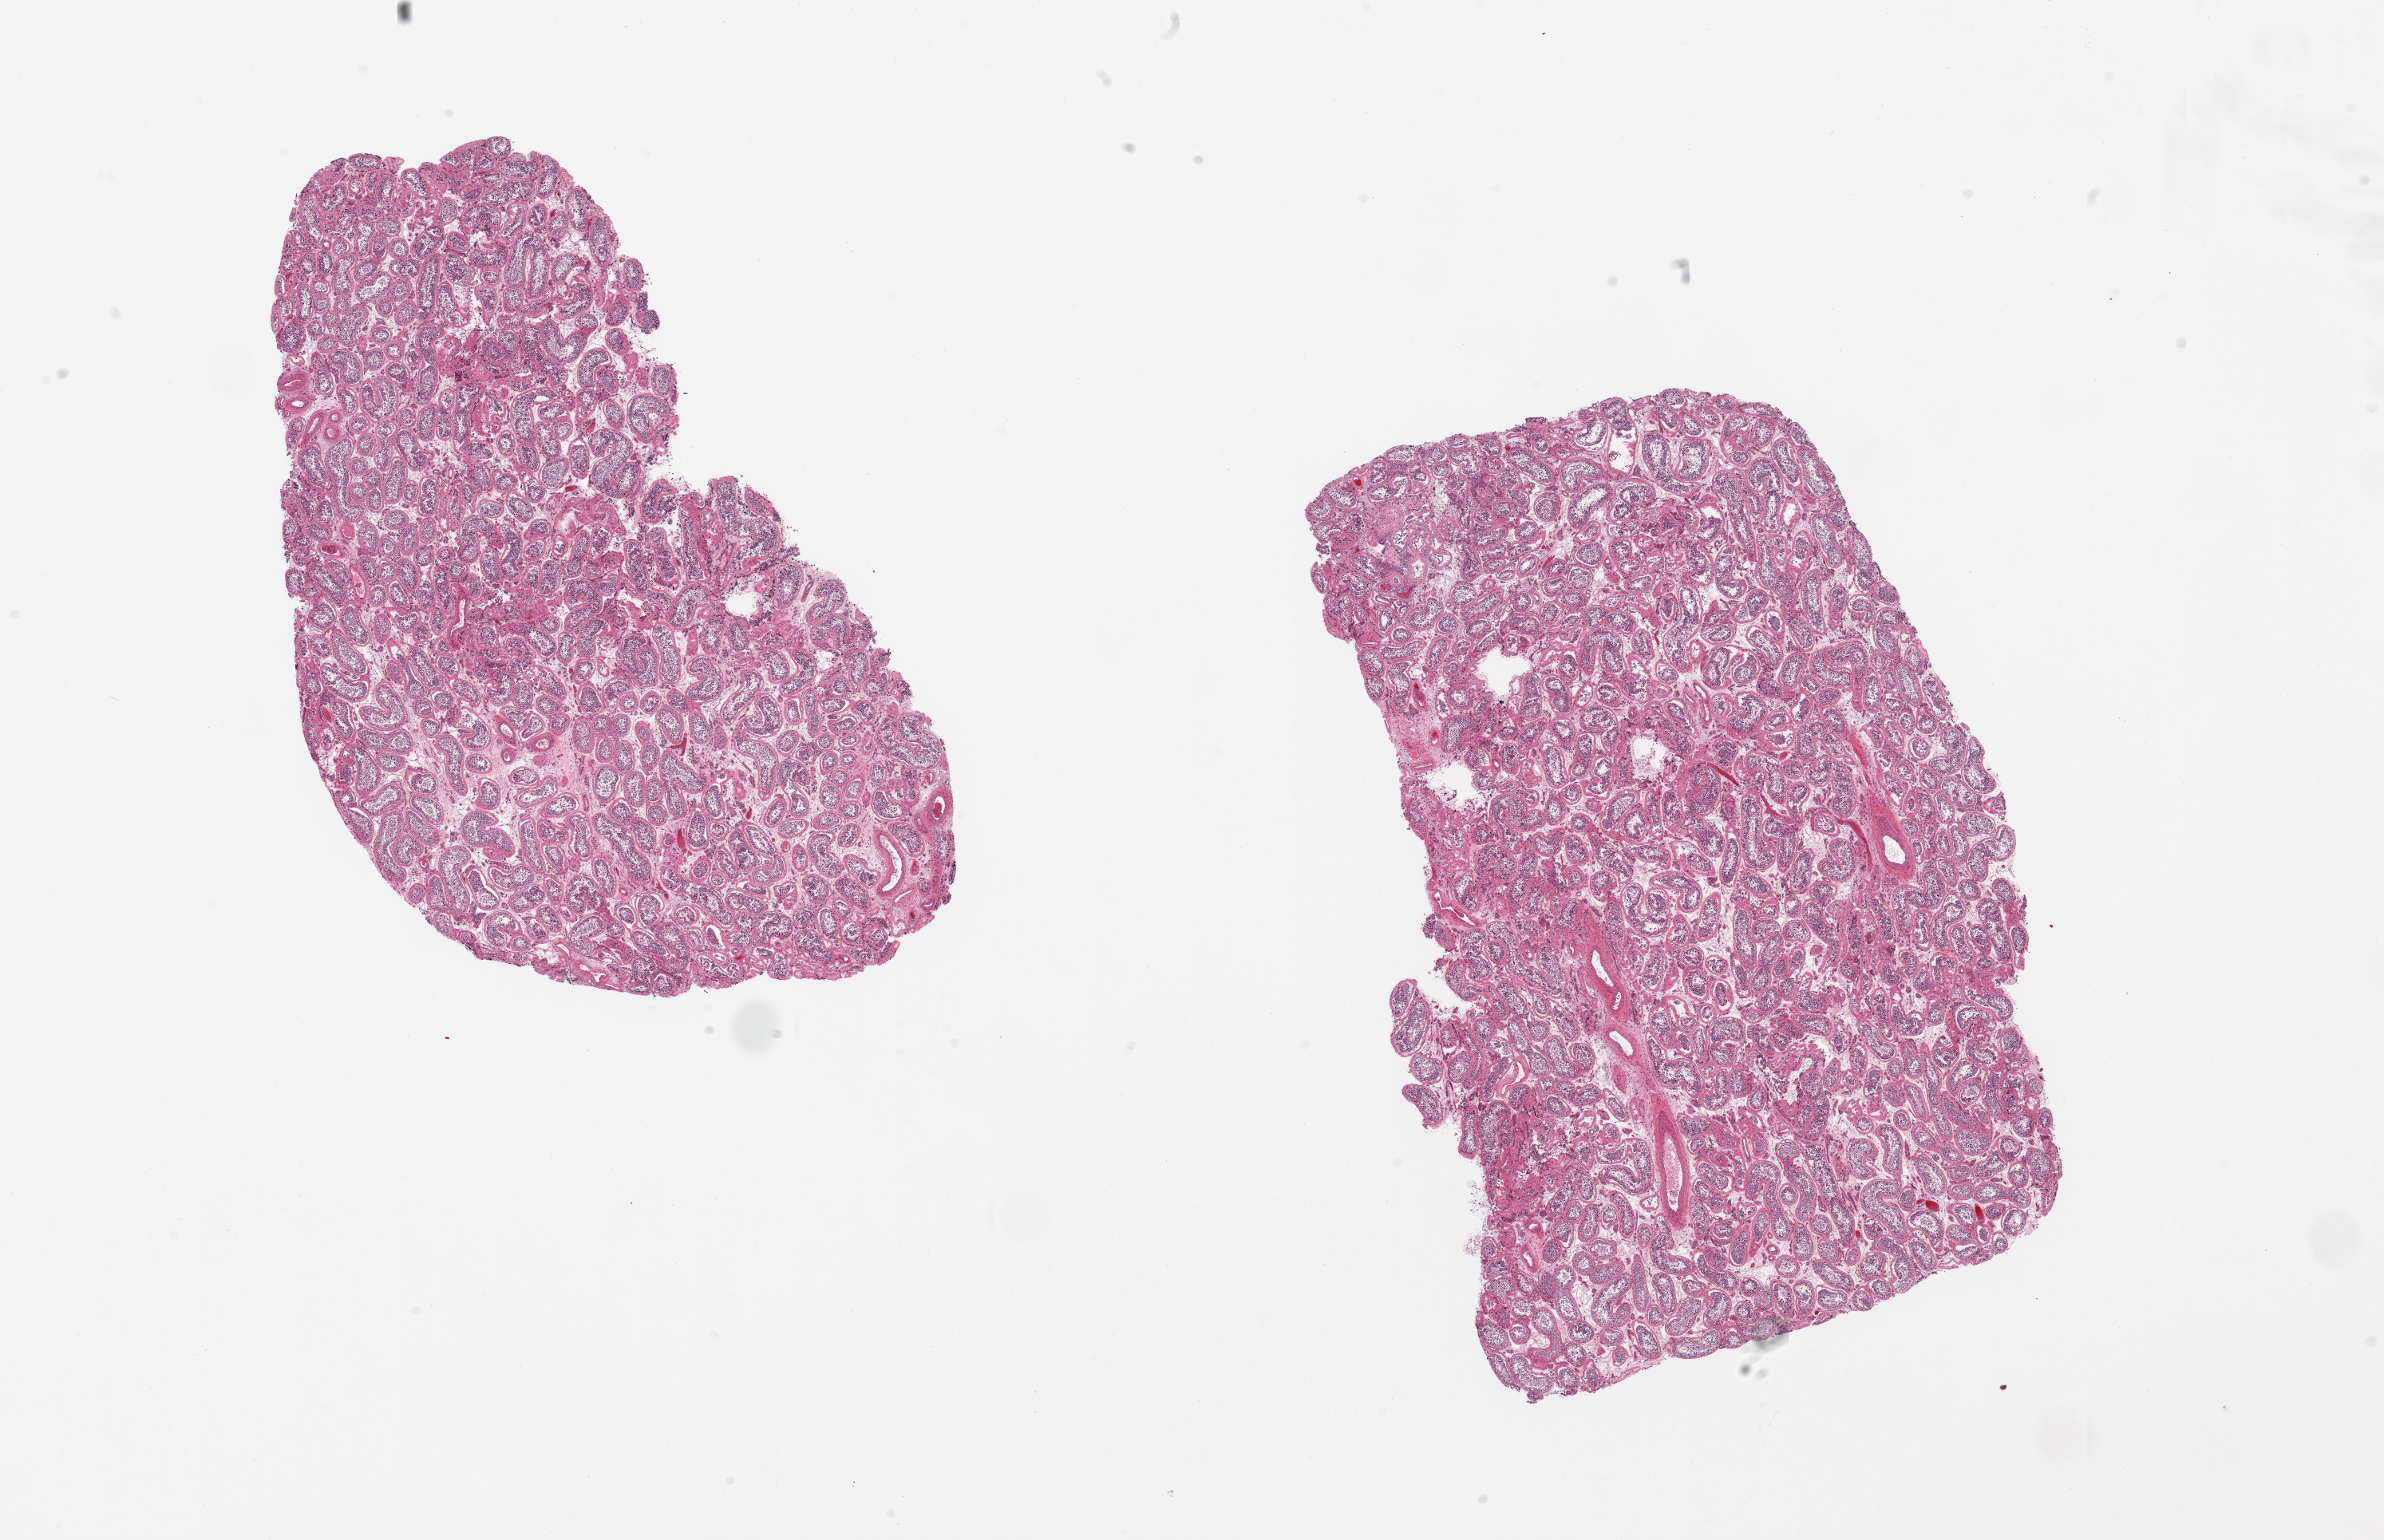
Whole-slide image, haematoxylin and eosin stain, whole scanned area (about 23.6 x 15.3 mm) shown as a low-resolution overview, PAXgene-fixed, paraffin-embedded tissue, target tissue: testis, donor tissue sample. Donor sex: male.
Pathologist's review note for this sample: 2 pieces, spermatogenesis appears reduced.